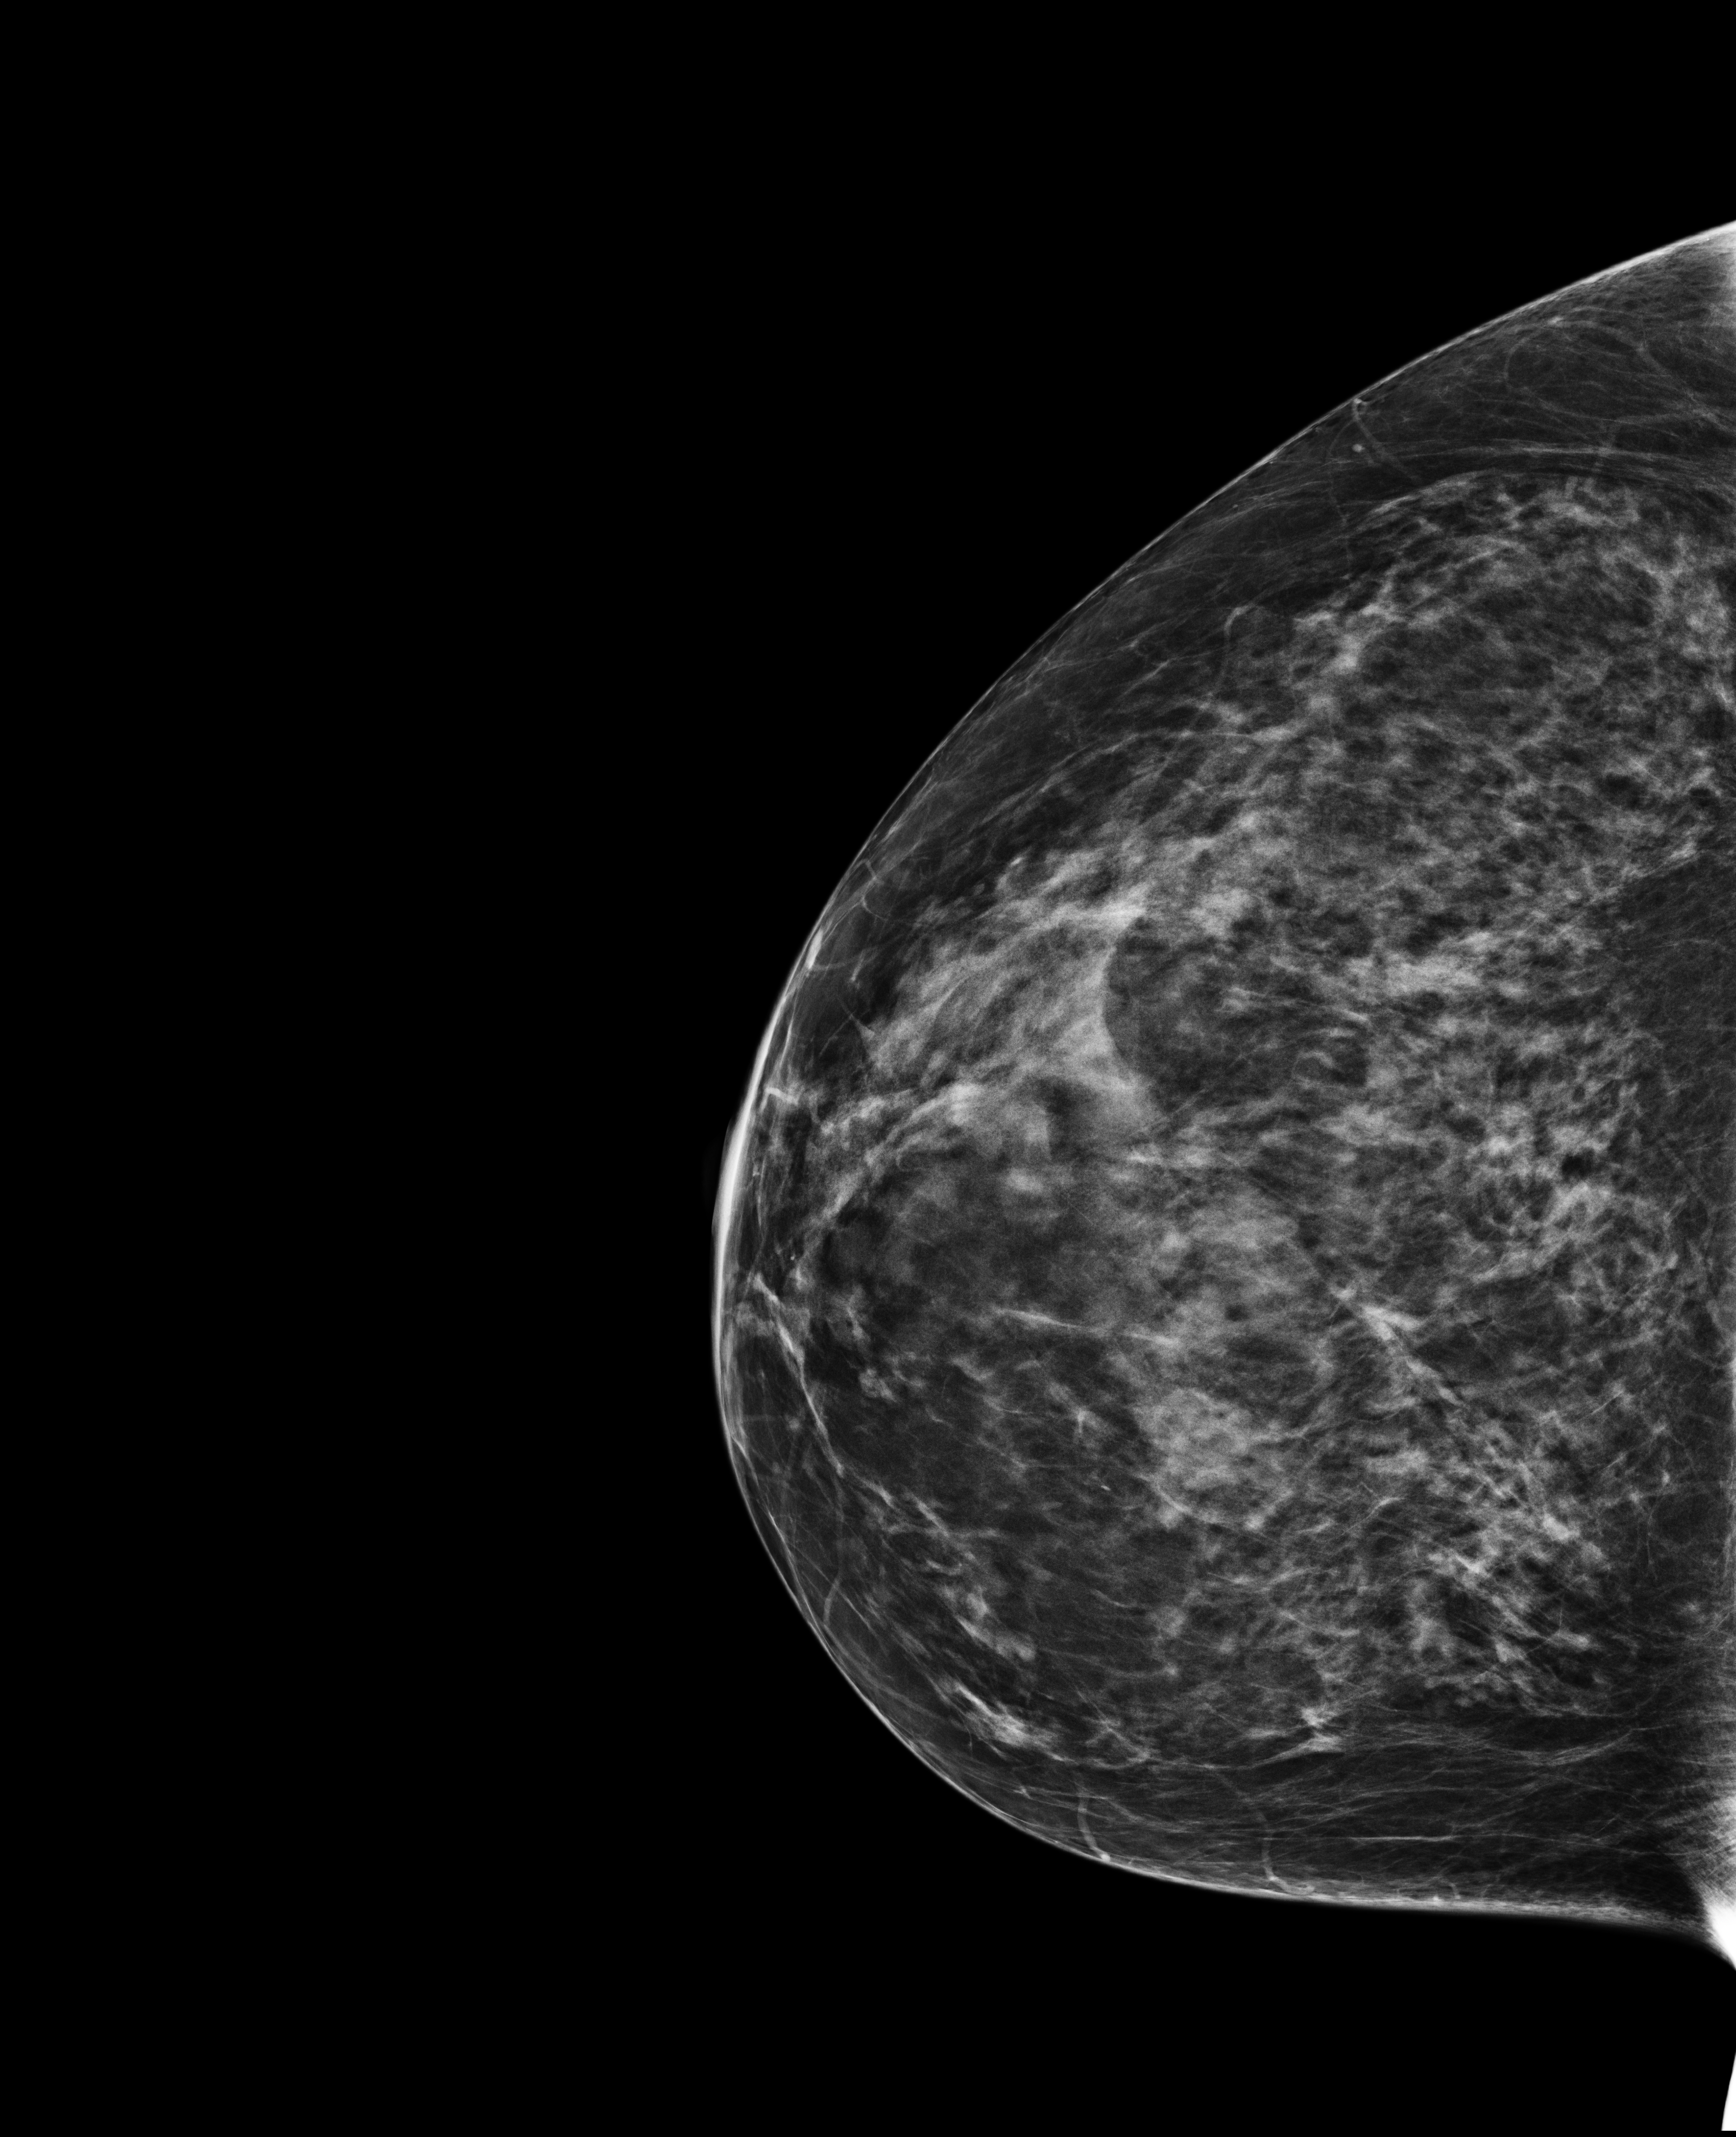
Screening examination, compressed breast thickness 63 mm, system: Selenia Dimensions. Female patient, age 61 years.
Image type: full-field digital mammogram. Breast: right. Projection: craniocaudal (CC) view.